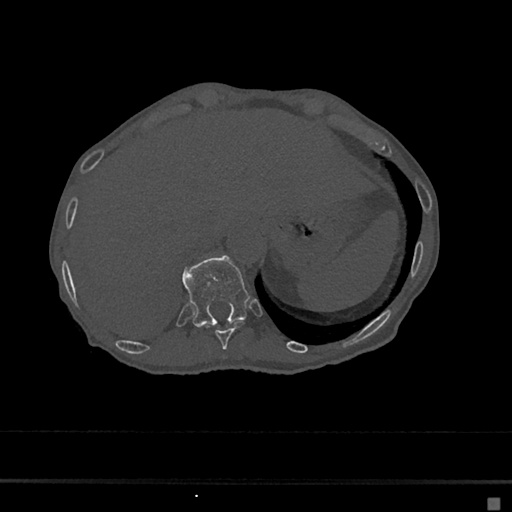
CT including the spine, one axial slice. Position 191 of 797 along the scan axis. Reconstruction kernel Br40s/3. 120 kVp. Bone window (W 1800 / L 400 HU). 0.5 mm slice thickness. 512 × 512 image matrix, field of view 360 × 360 mm. Female patient, age 68 years. From the clinical record (not read from this slice): primary cancer: renal.
Structures marked on this image (semi-automatically segmented with operator editing):
- T10 vertebra: bounding box [x1, y1, x2, y2] px = [206, 321, 244, 350]
- T11 vertebra: [183, 256, 250, 326]